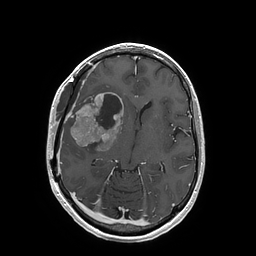
Brain MRI from a brain-tumour surgery series, one axial slice. T1-weighted post-contrast. 1 mm slice thickness. 256 × 256 image matrix, field of view 250 × 250 mm. From the clinical record (not read from this slice): histopathology: Glioblastoma; WHO grade: 4; IDH mutation: no; tumour location: Right Insular.
Outlined on this slice (expert manual segmentation):
- tumour: bounding box (x1, y1, x2, y2) in pixels: (70, 92, 123, 151)